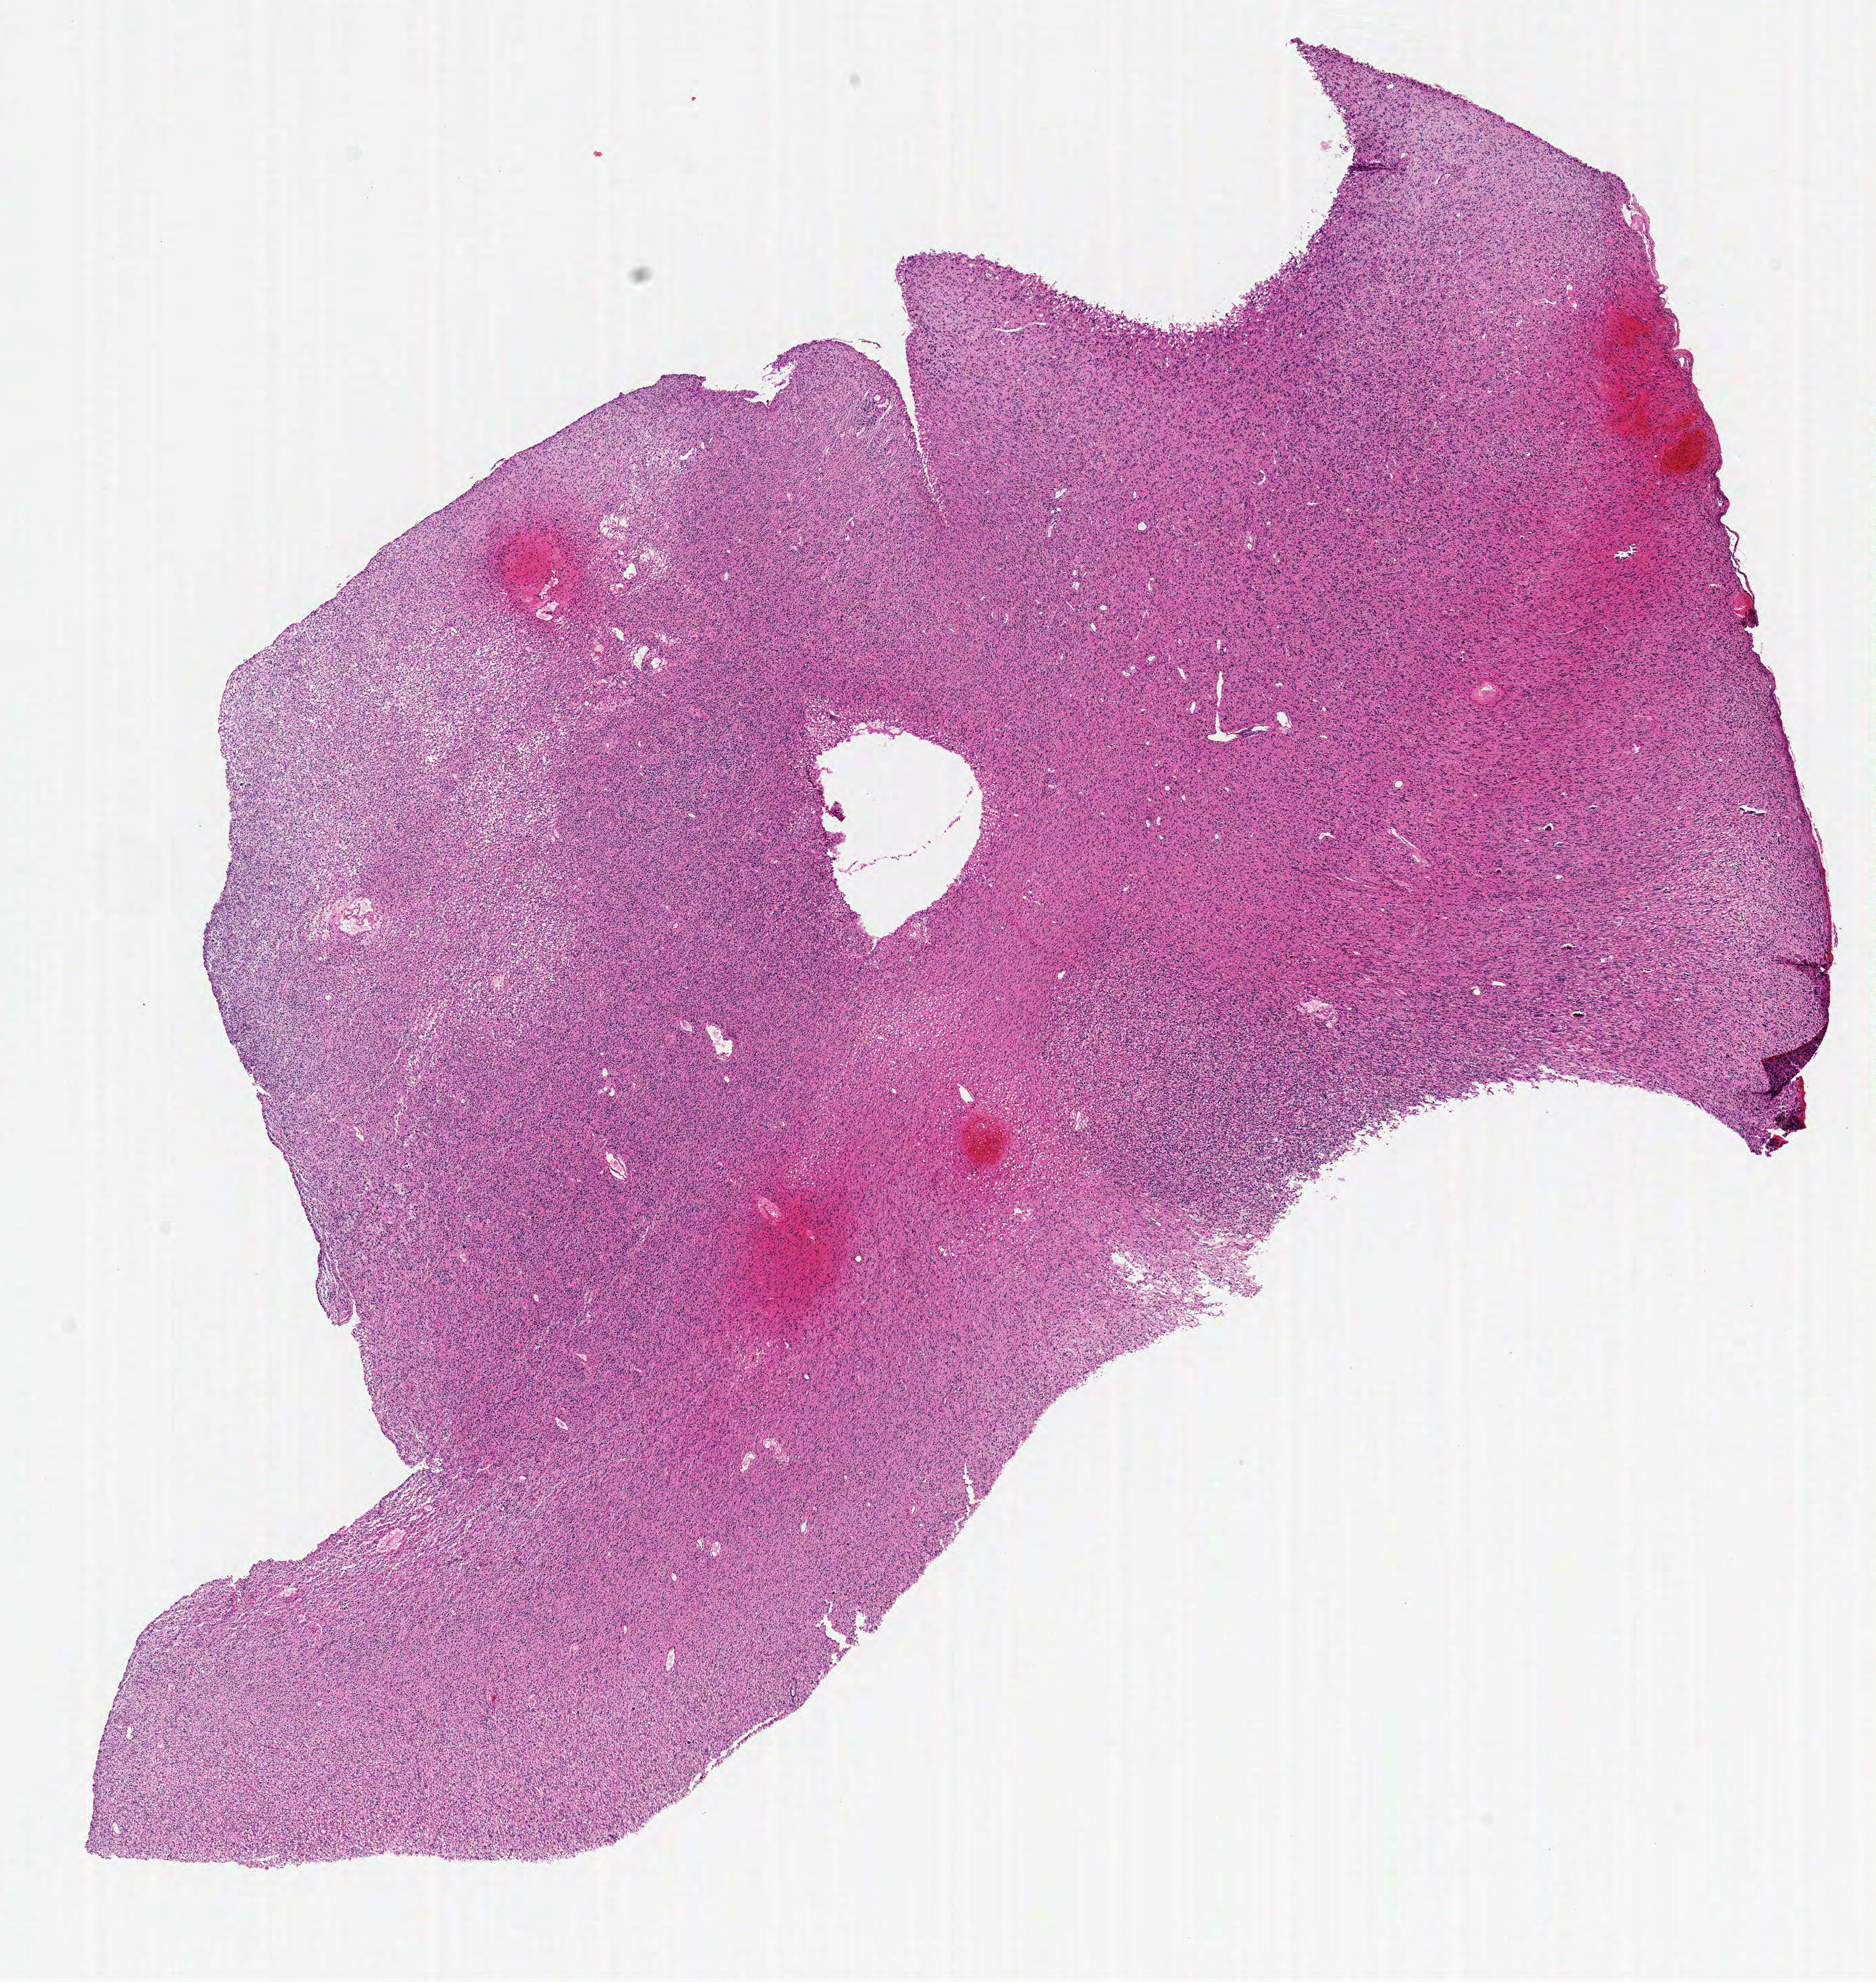
Digitized H&E tissue section (whole slide), shown as a low-resolution overview of the whole scanned area (about 11.0 x 11.6 mm, acquisition: 20x scan); formalin-fixed paraffin-embedded (FFPE) diagnostic section; brain, primary tumour sample. Patient: male, age at initial diagnosis 60 years.
Pathologic diagnosis: Glioblastoma.